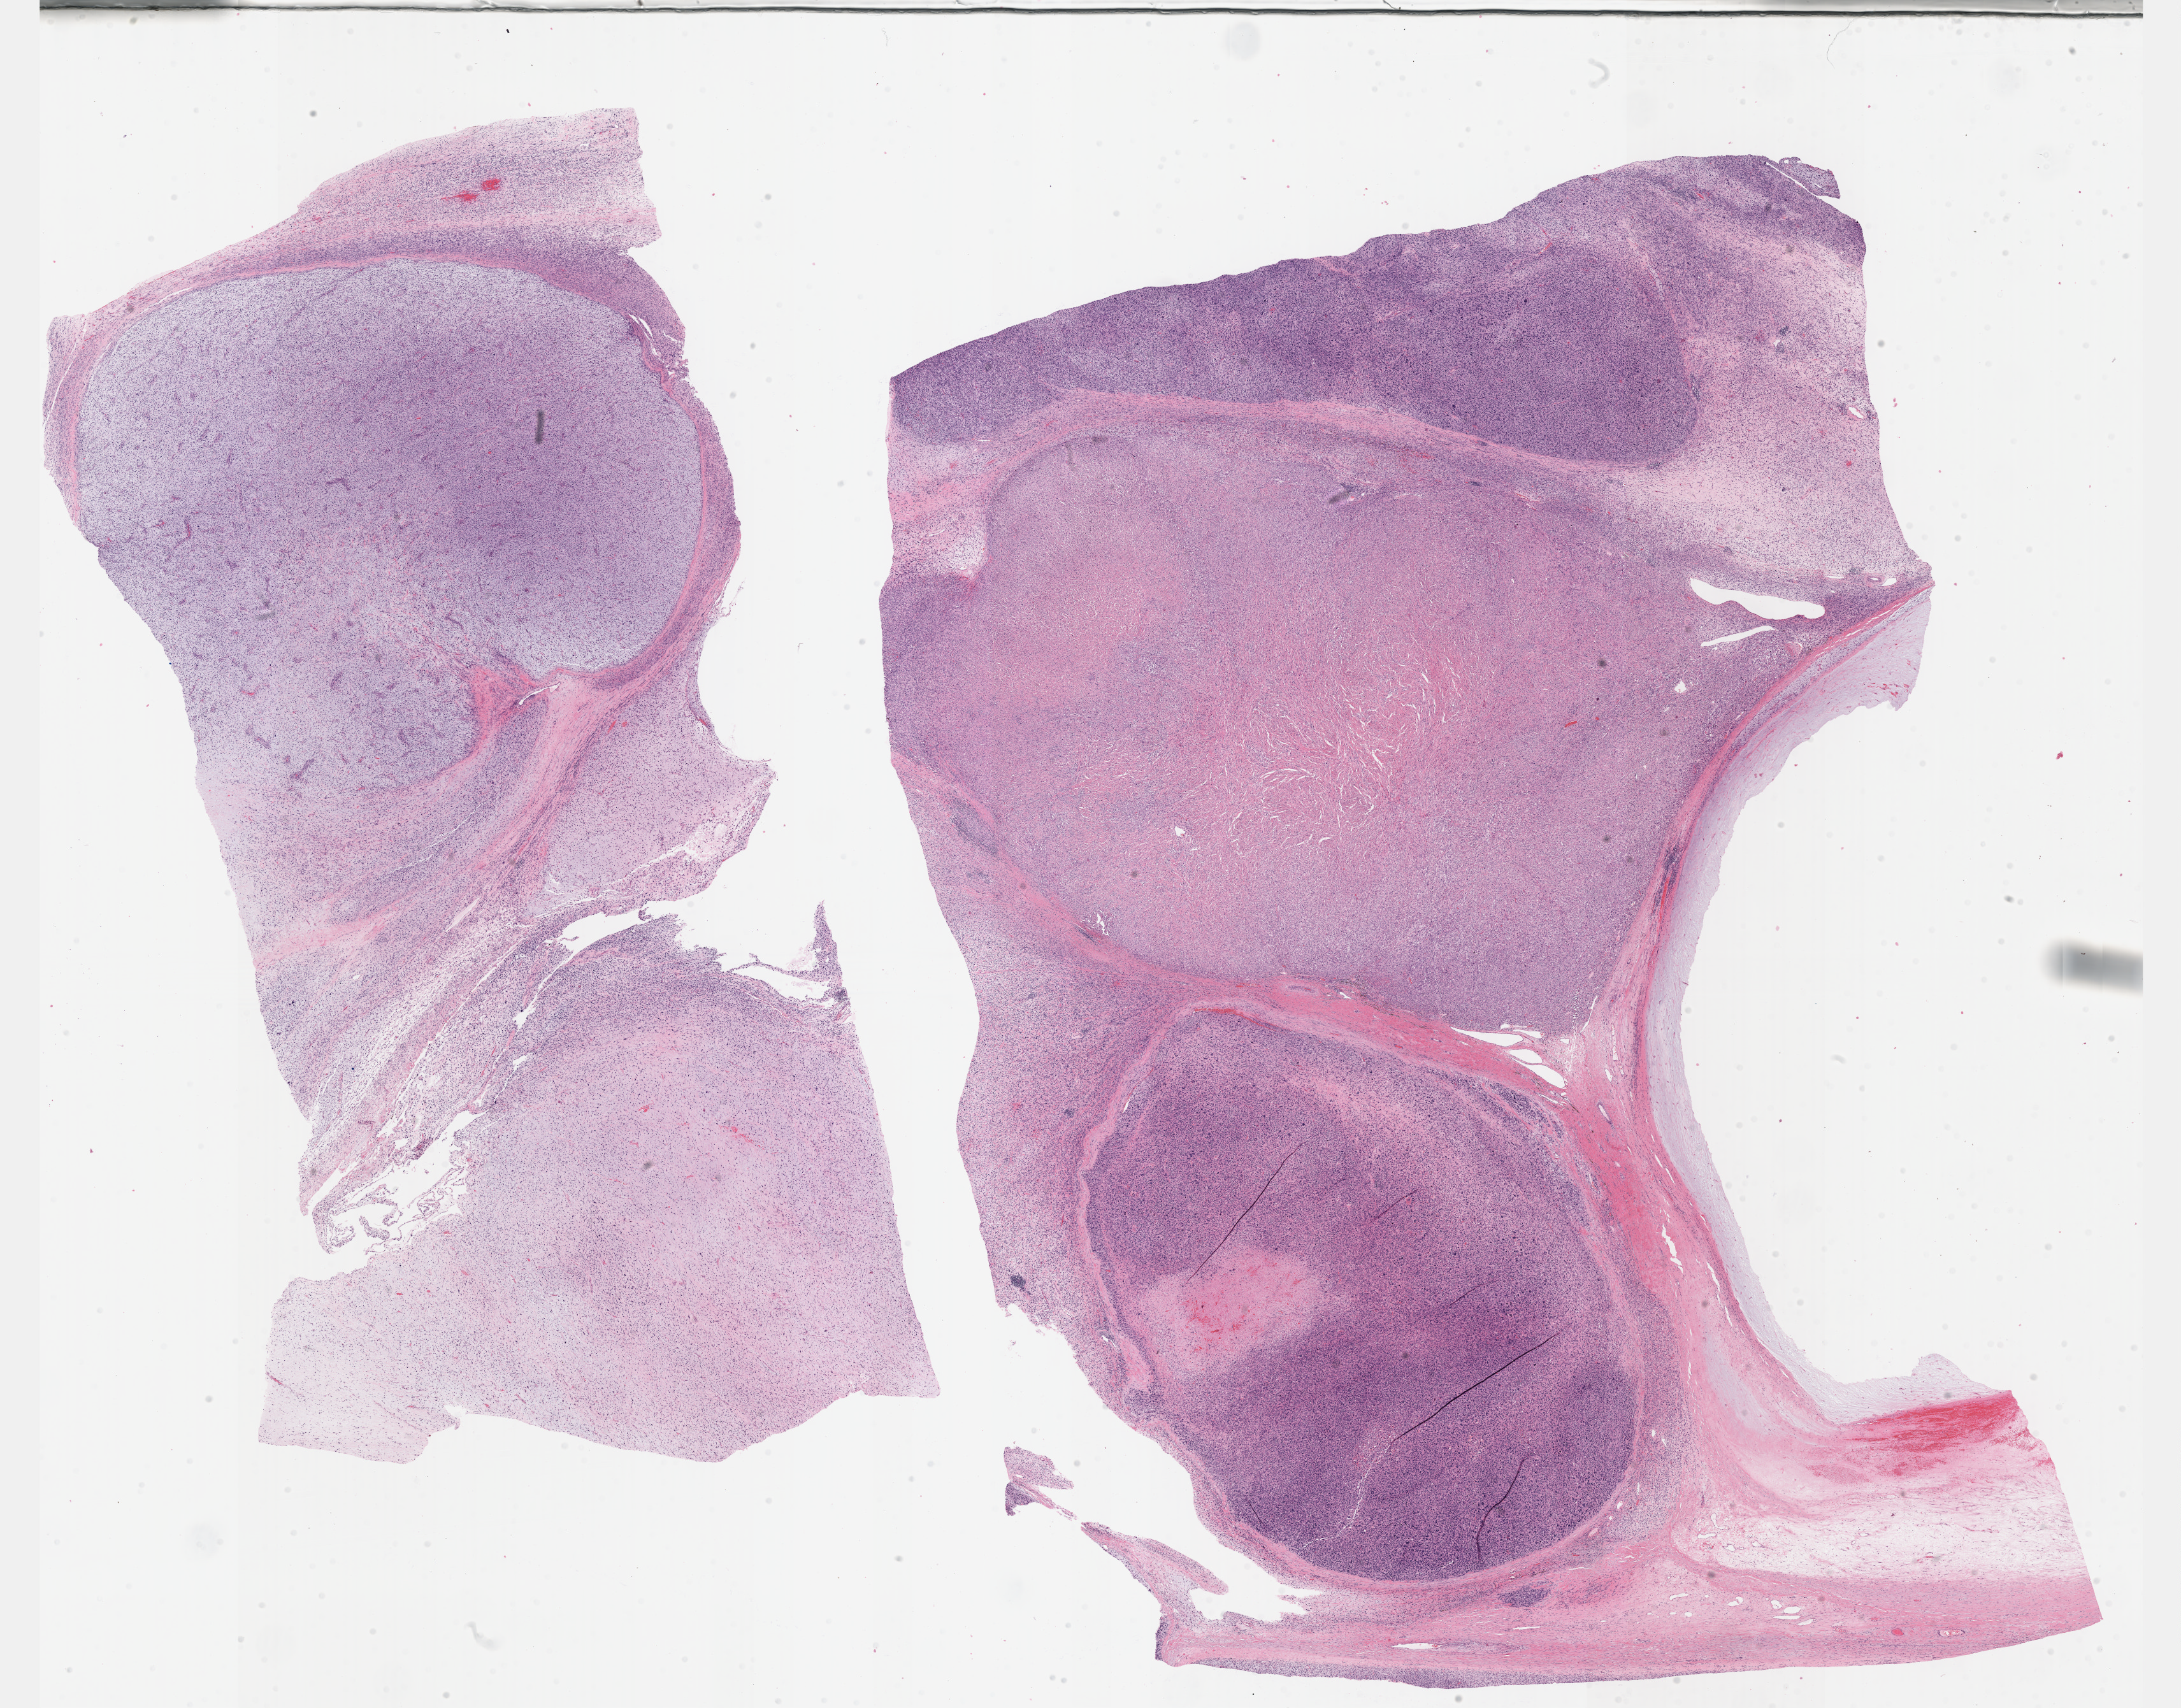
H&E whole-slide image — low-resolution overview of the scanned area, about 27.7 x 21.7 mm (acquisition: 40x scan), formalin-fixed paraffin-embedded (FFPE) diagnostic section, primary tumour sample from the connective, subcutaneous and other soft tissues. Male patient.
Diagnosis: Fibromyxosarcoma (connective, subcutaneous and other soft tissues of lower limb and hip).